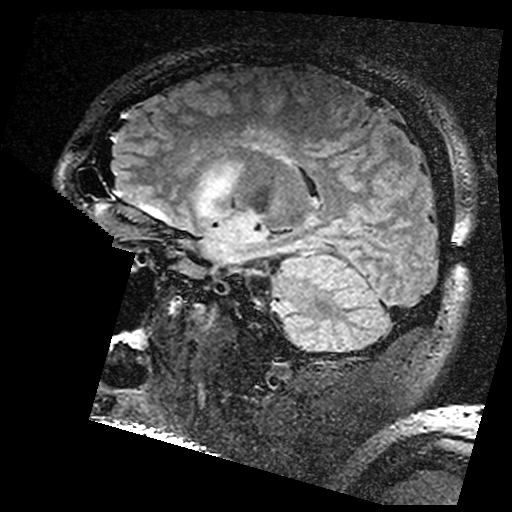
Brain MRI from a brain-tumour surgery series, one sagittal slice; slice 108 of 176 in the series (ordered by position); T2 FLAIR; 1 mm slice thickness; 512 × 512 image matrix, field of view 250 × 250 mm. From the clinical record (not read from this slice): histopathology: Astrocytoma; WHO grade: 3; IDH mutation: yes; tumour location: Left Insular.
Outlined on this slice (outlined manually by an expert reader):
- residual tumour: bounding box (x1, y1, x2, y2) in pixels: (204, 160, 238, 198)